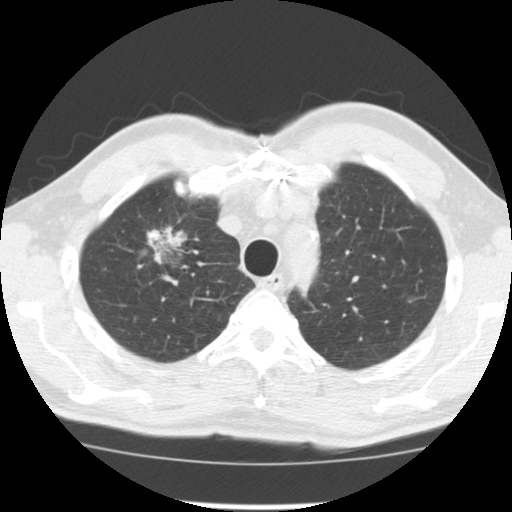
Chest CT (low-dose screening protocol), one axial image, third screening round (two years after baseline), lung window (W 1500 / L -600 HU), 2.5 mm slice thickness, standard (soft-tissue) reconstruction kernel (STANDARD), 120 kVp, slice 28 of 128 in the series. Male participant, aged 64 years at enrolment. Former smoker at enrolment.
- Lesion marked by an expert reader, bounding box (x1, y1, x2, y2) in pixels: (127, 220, 204, 284).
- The screening reader recorded 3 non-calcified nodules or masses ≥4 mm on this exam (right upper lobe, right lower lobe, left upper lobe); which of them this box marks is not recorded.